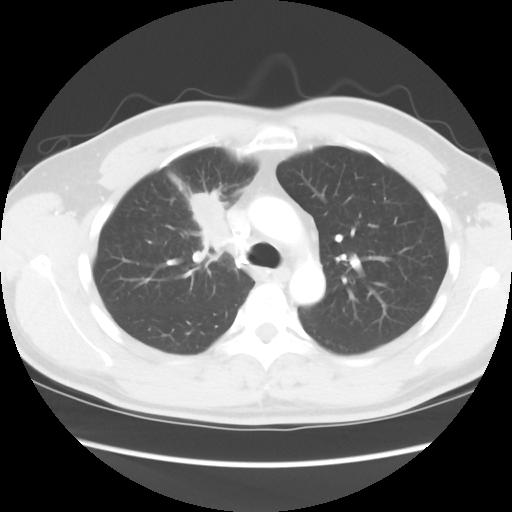
Chest CT, one axial slice. Position 63 of 80 along the scan axis. Reconstruction kernel STANDARD. Lung window (W 1500 / L -600 HU). 5 mm slice thickness. 512 × 512 image matrix, field of view 360 × 360 mm. Patient: male, 35 years. From the clinical record (not read from this slice): clinical TNM (as recorded): T1c N1 M1b.
Structures marked on this image (rectangle marked by the reading radiologist):
- lung tumour (recorded histology: adenocarcinoma): bounding box (x1, y1, x2, y2) in pixels: (189, 191, 237, 255)